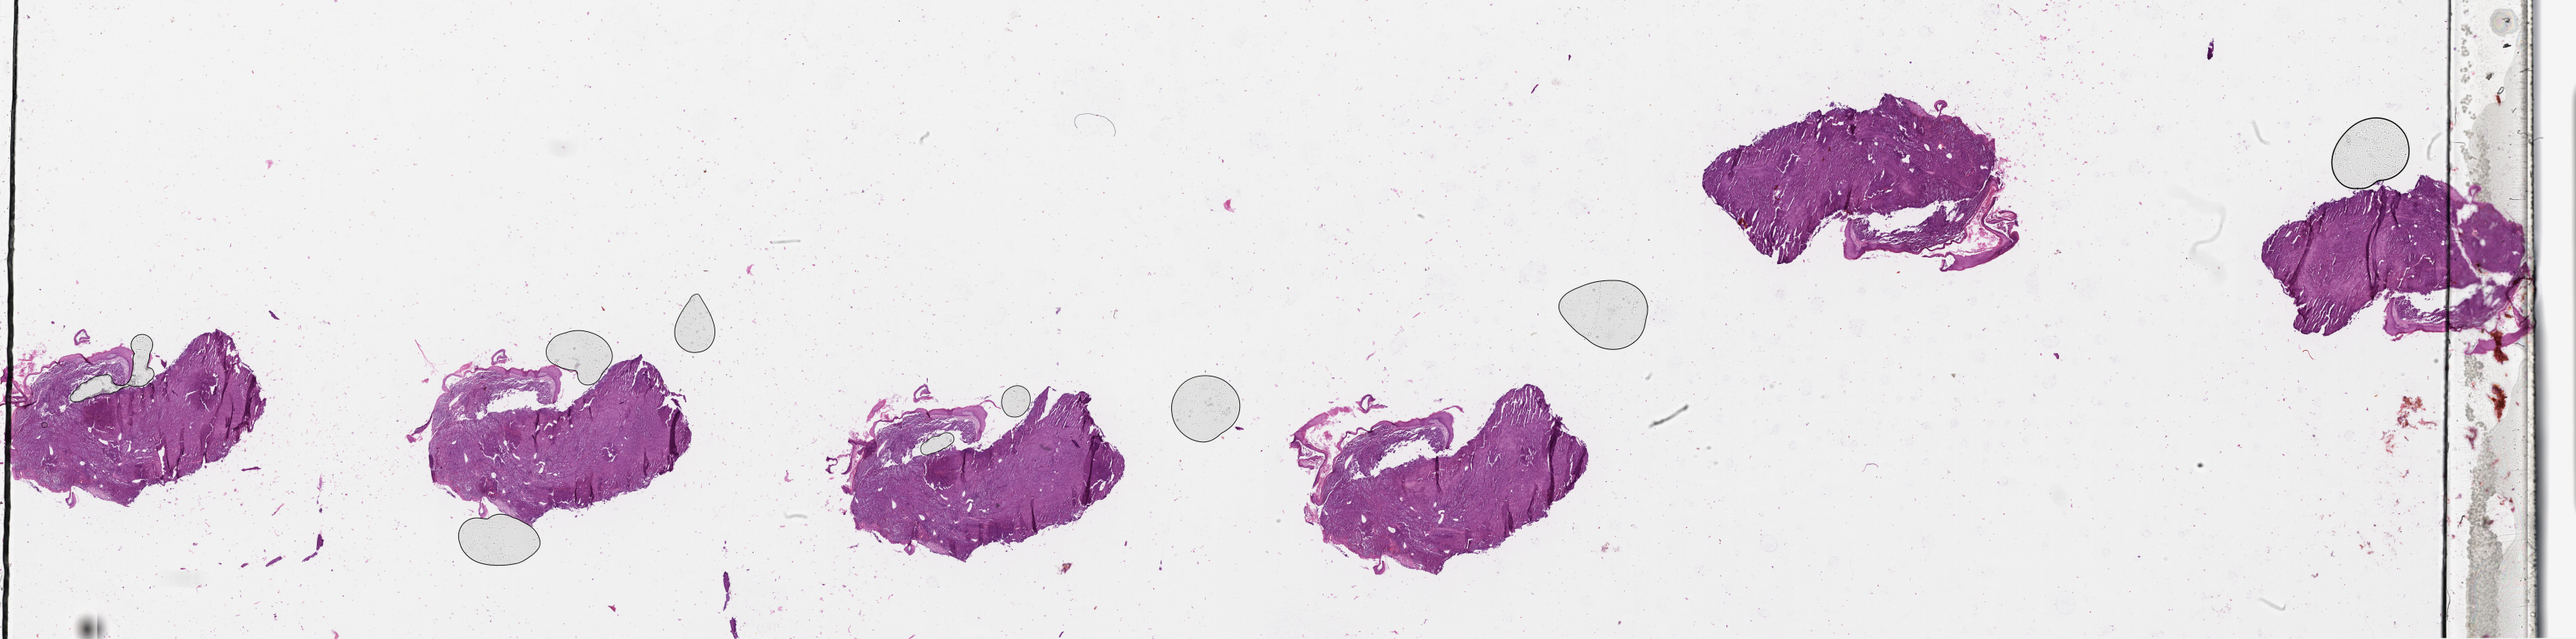
Whole-slide histology image, H&E, shown as a low-resolution overview of the whole scanned area (about 53.1 x 13.2 mm).
Patient diagnosis (cohort enrolment): cutaneous melanoma (skin).